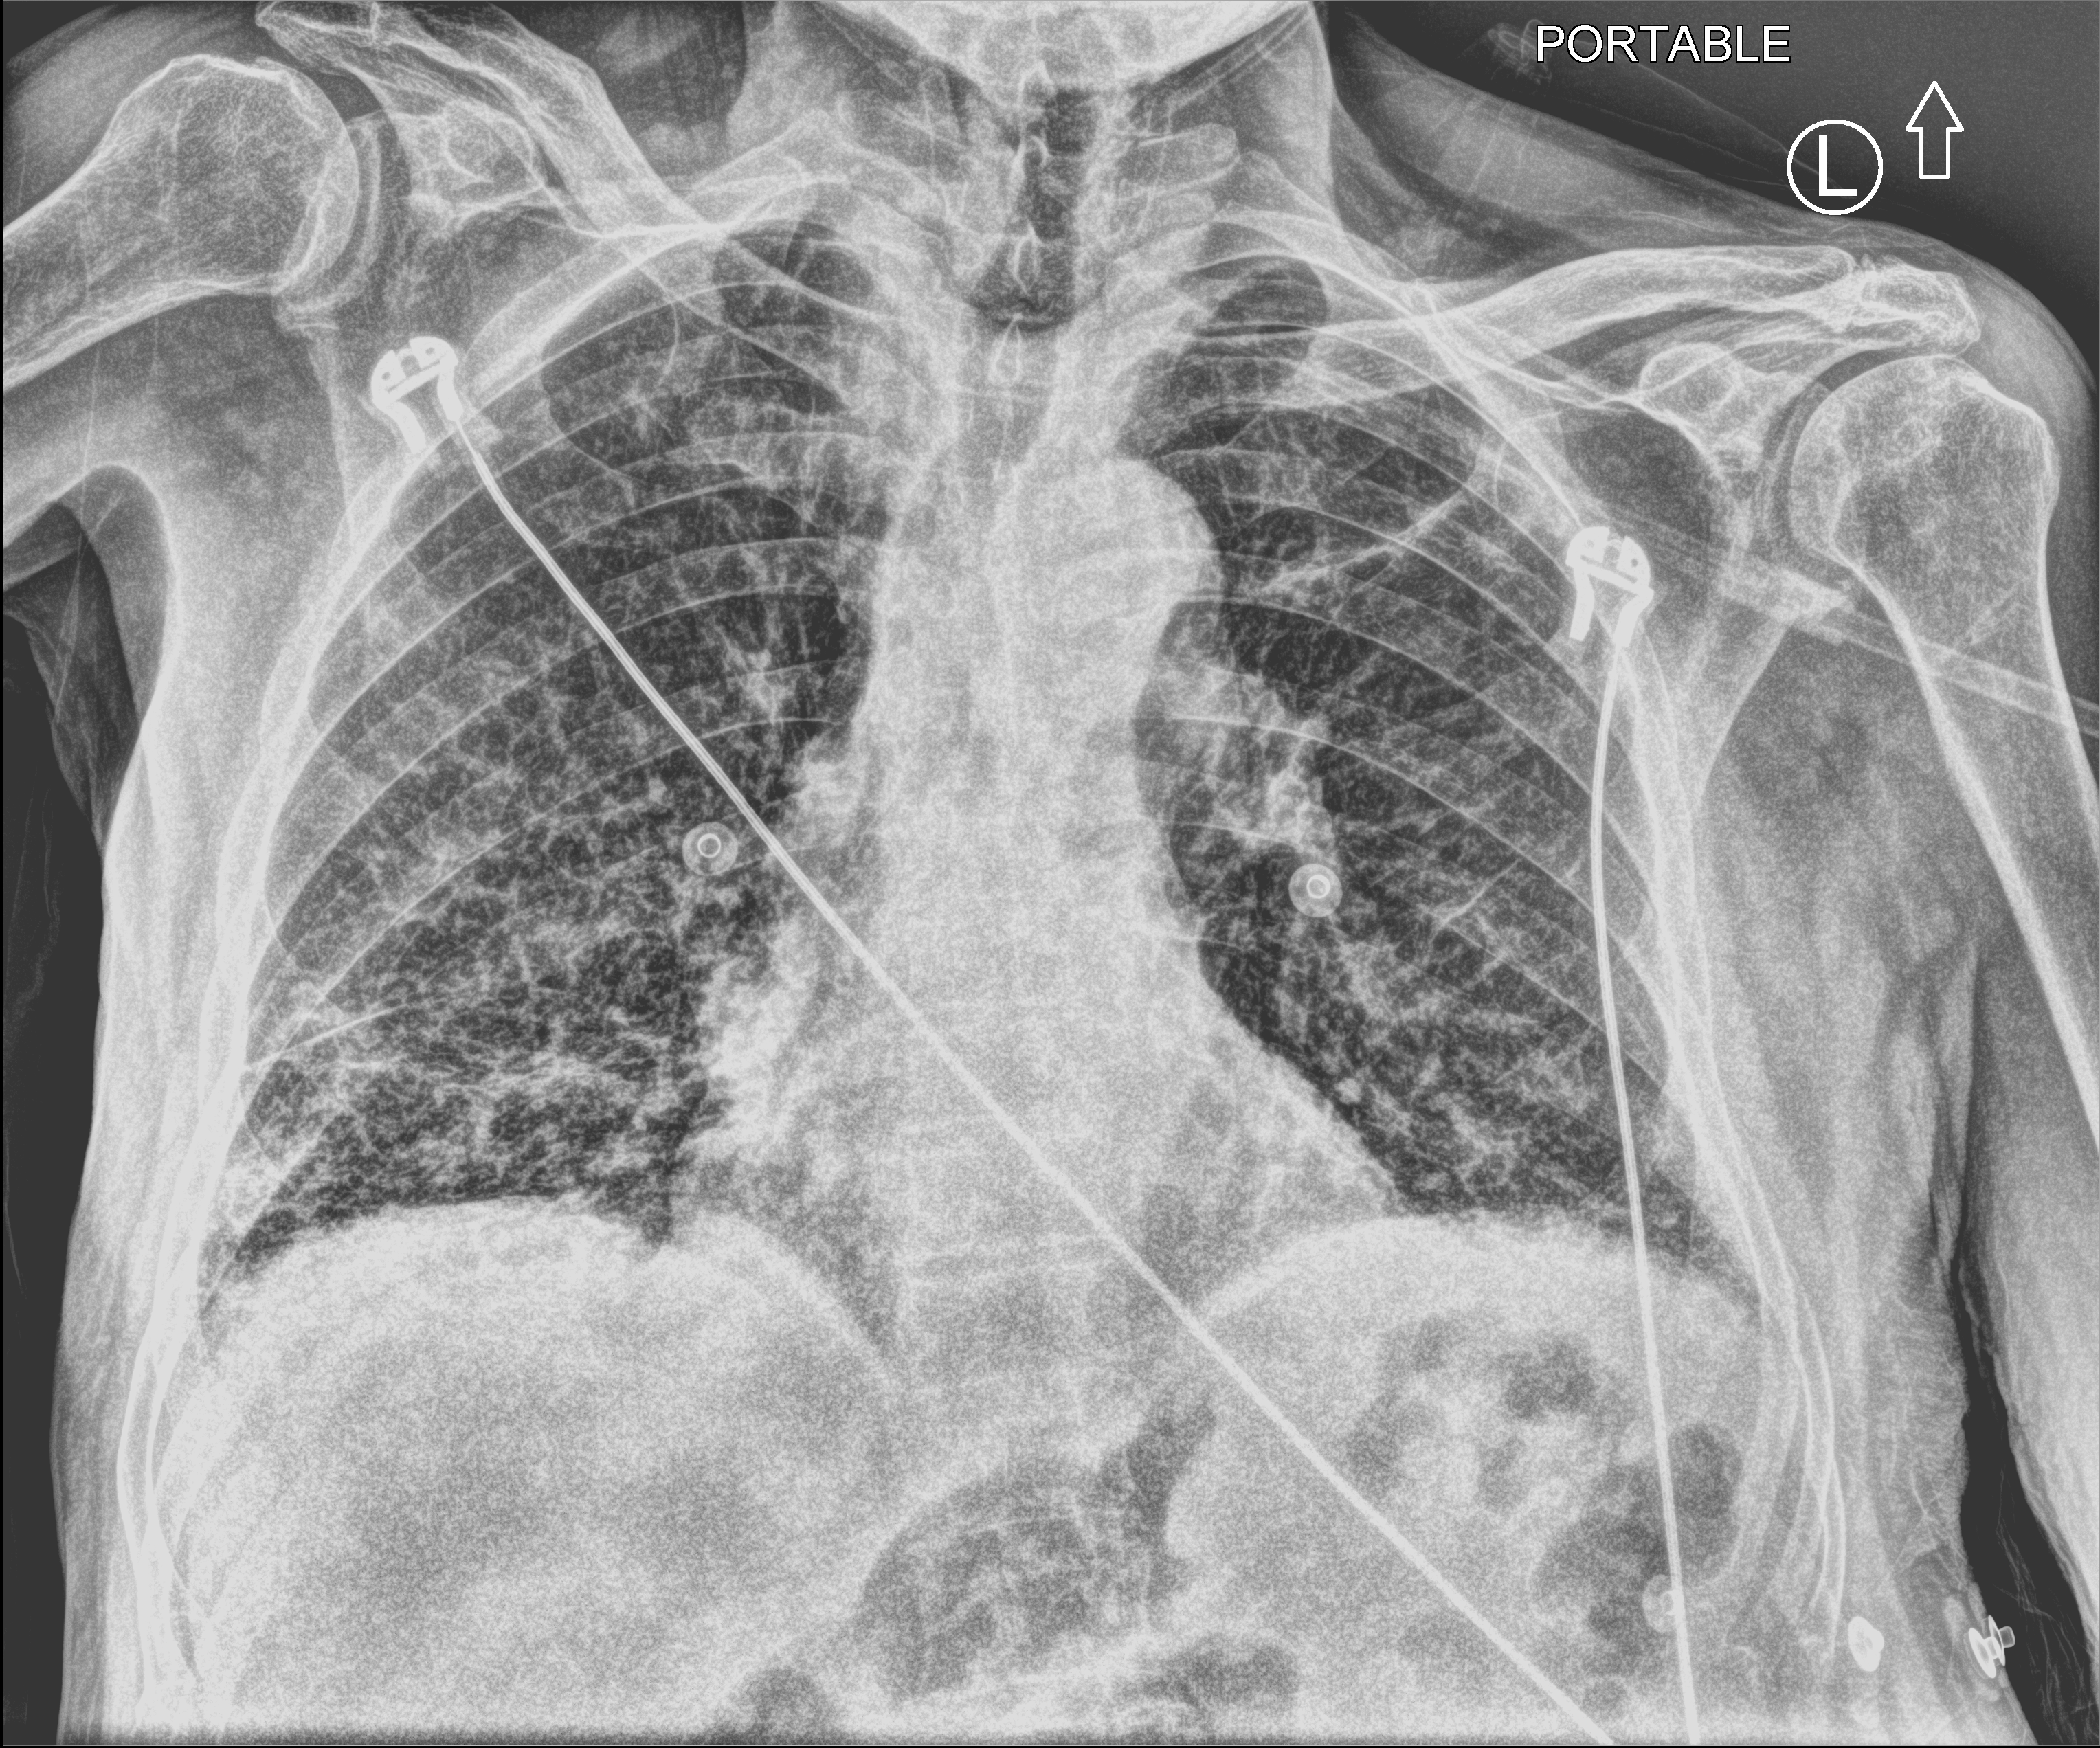
Portable chest radiograph, anteroposterior (AP) projection. Patient hospitalised with COVID-19; male, aged 75–90 years.
Hospital-stay facts (about this admission, not read from this image; timing relative to this image not recorded): admitted to intensive care during this hospital stay: no.